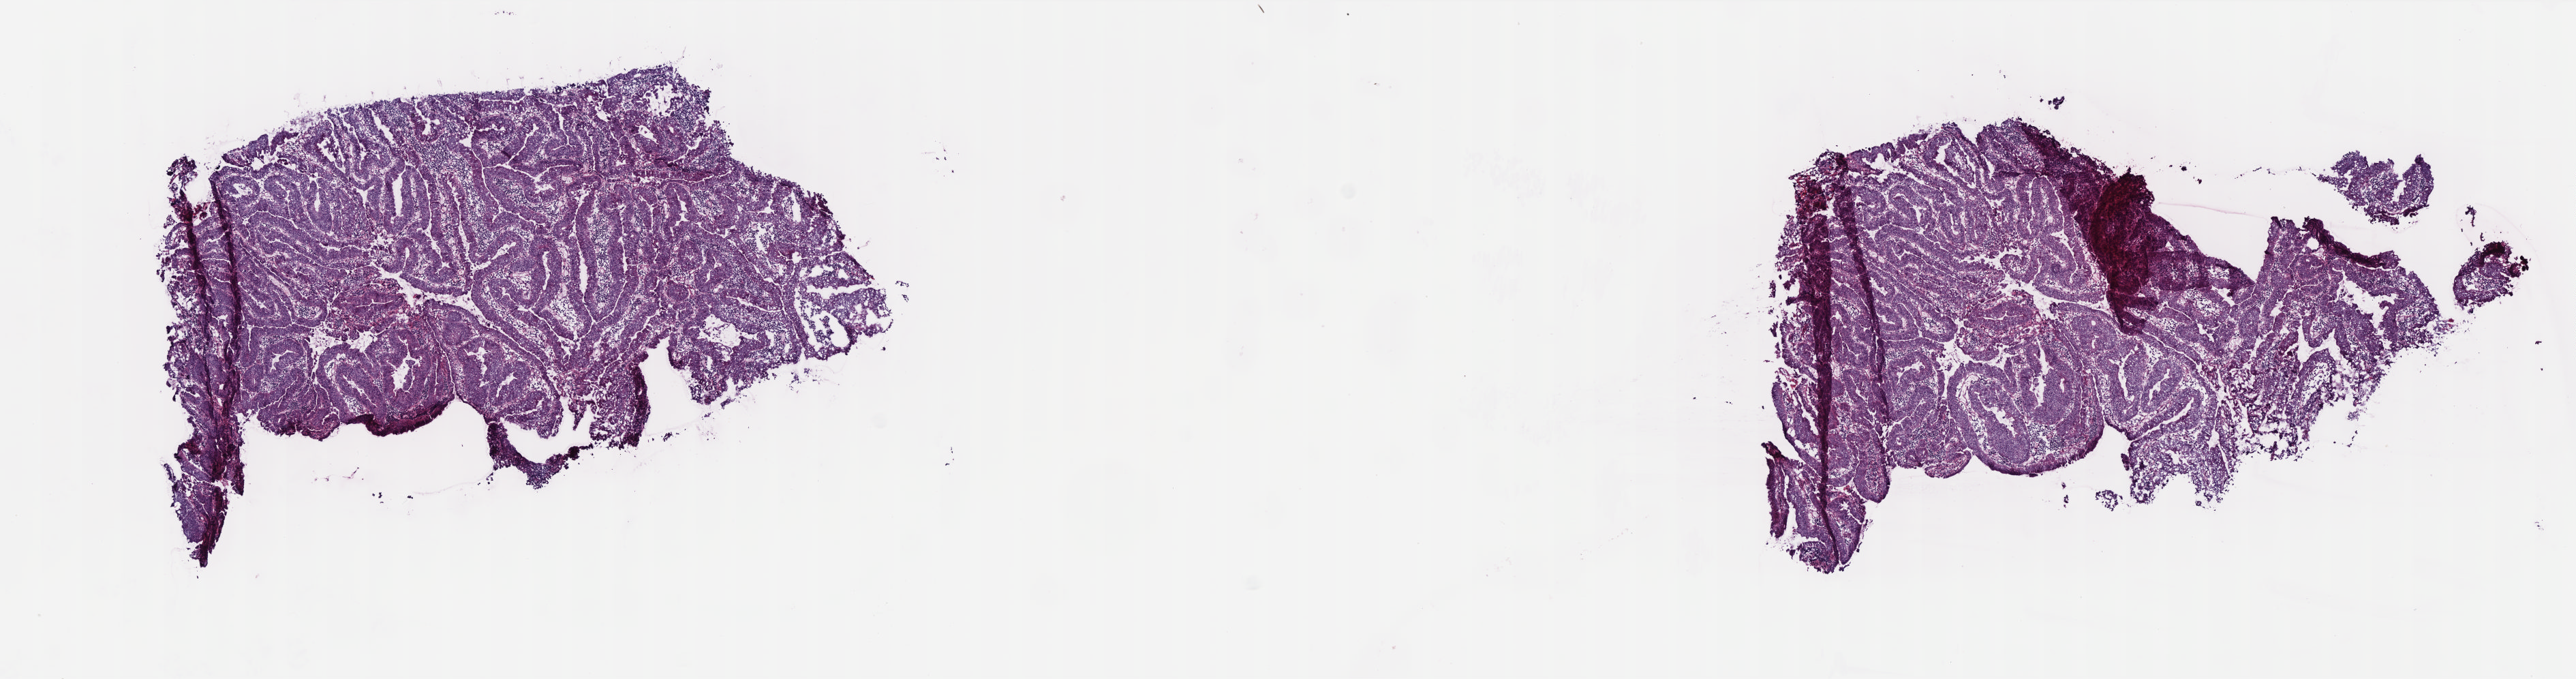
Whole-slide histology image, H&E — a low-resolution overview of the entire scanned area, about 15.2 x 4.0 mm. Frozen section. Colon, primary tumour sample. Patient: male, age at initial diagnosis 80 years. Composition of this section per pathologist review: tumour cells 99%, tumour nuclei 80%, normal cells 0%, stromal cells 0%, necrosis 1%. Inflammatory infiltration, as recorded: lymphocyte infiltration 15%, monocyte infiltration 2%, neutrophil infiltration 0%.
• diagnosis: Adenocarcinoma, NOS (sigmoid colon)
• AJCC pathologic stage: I (6th edition)